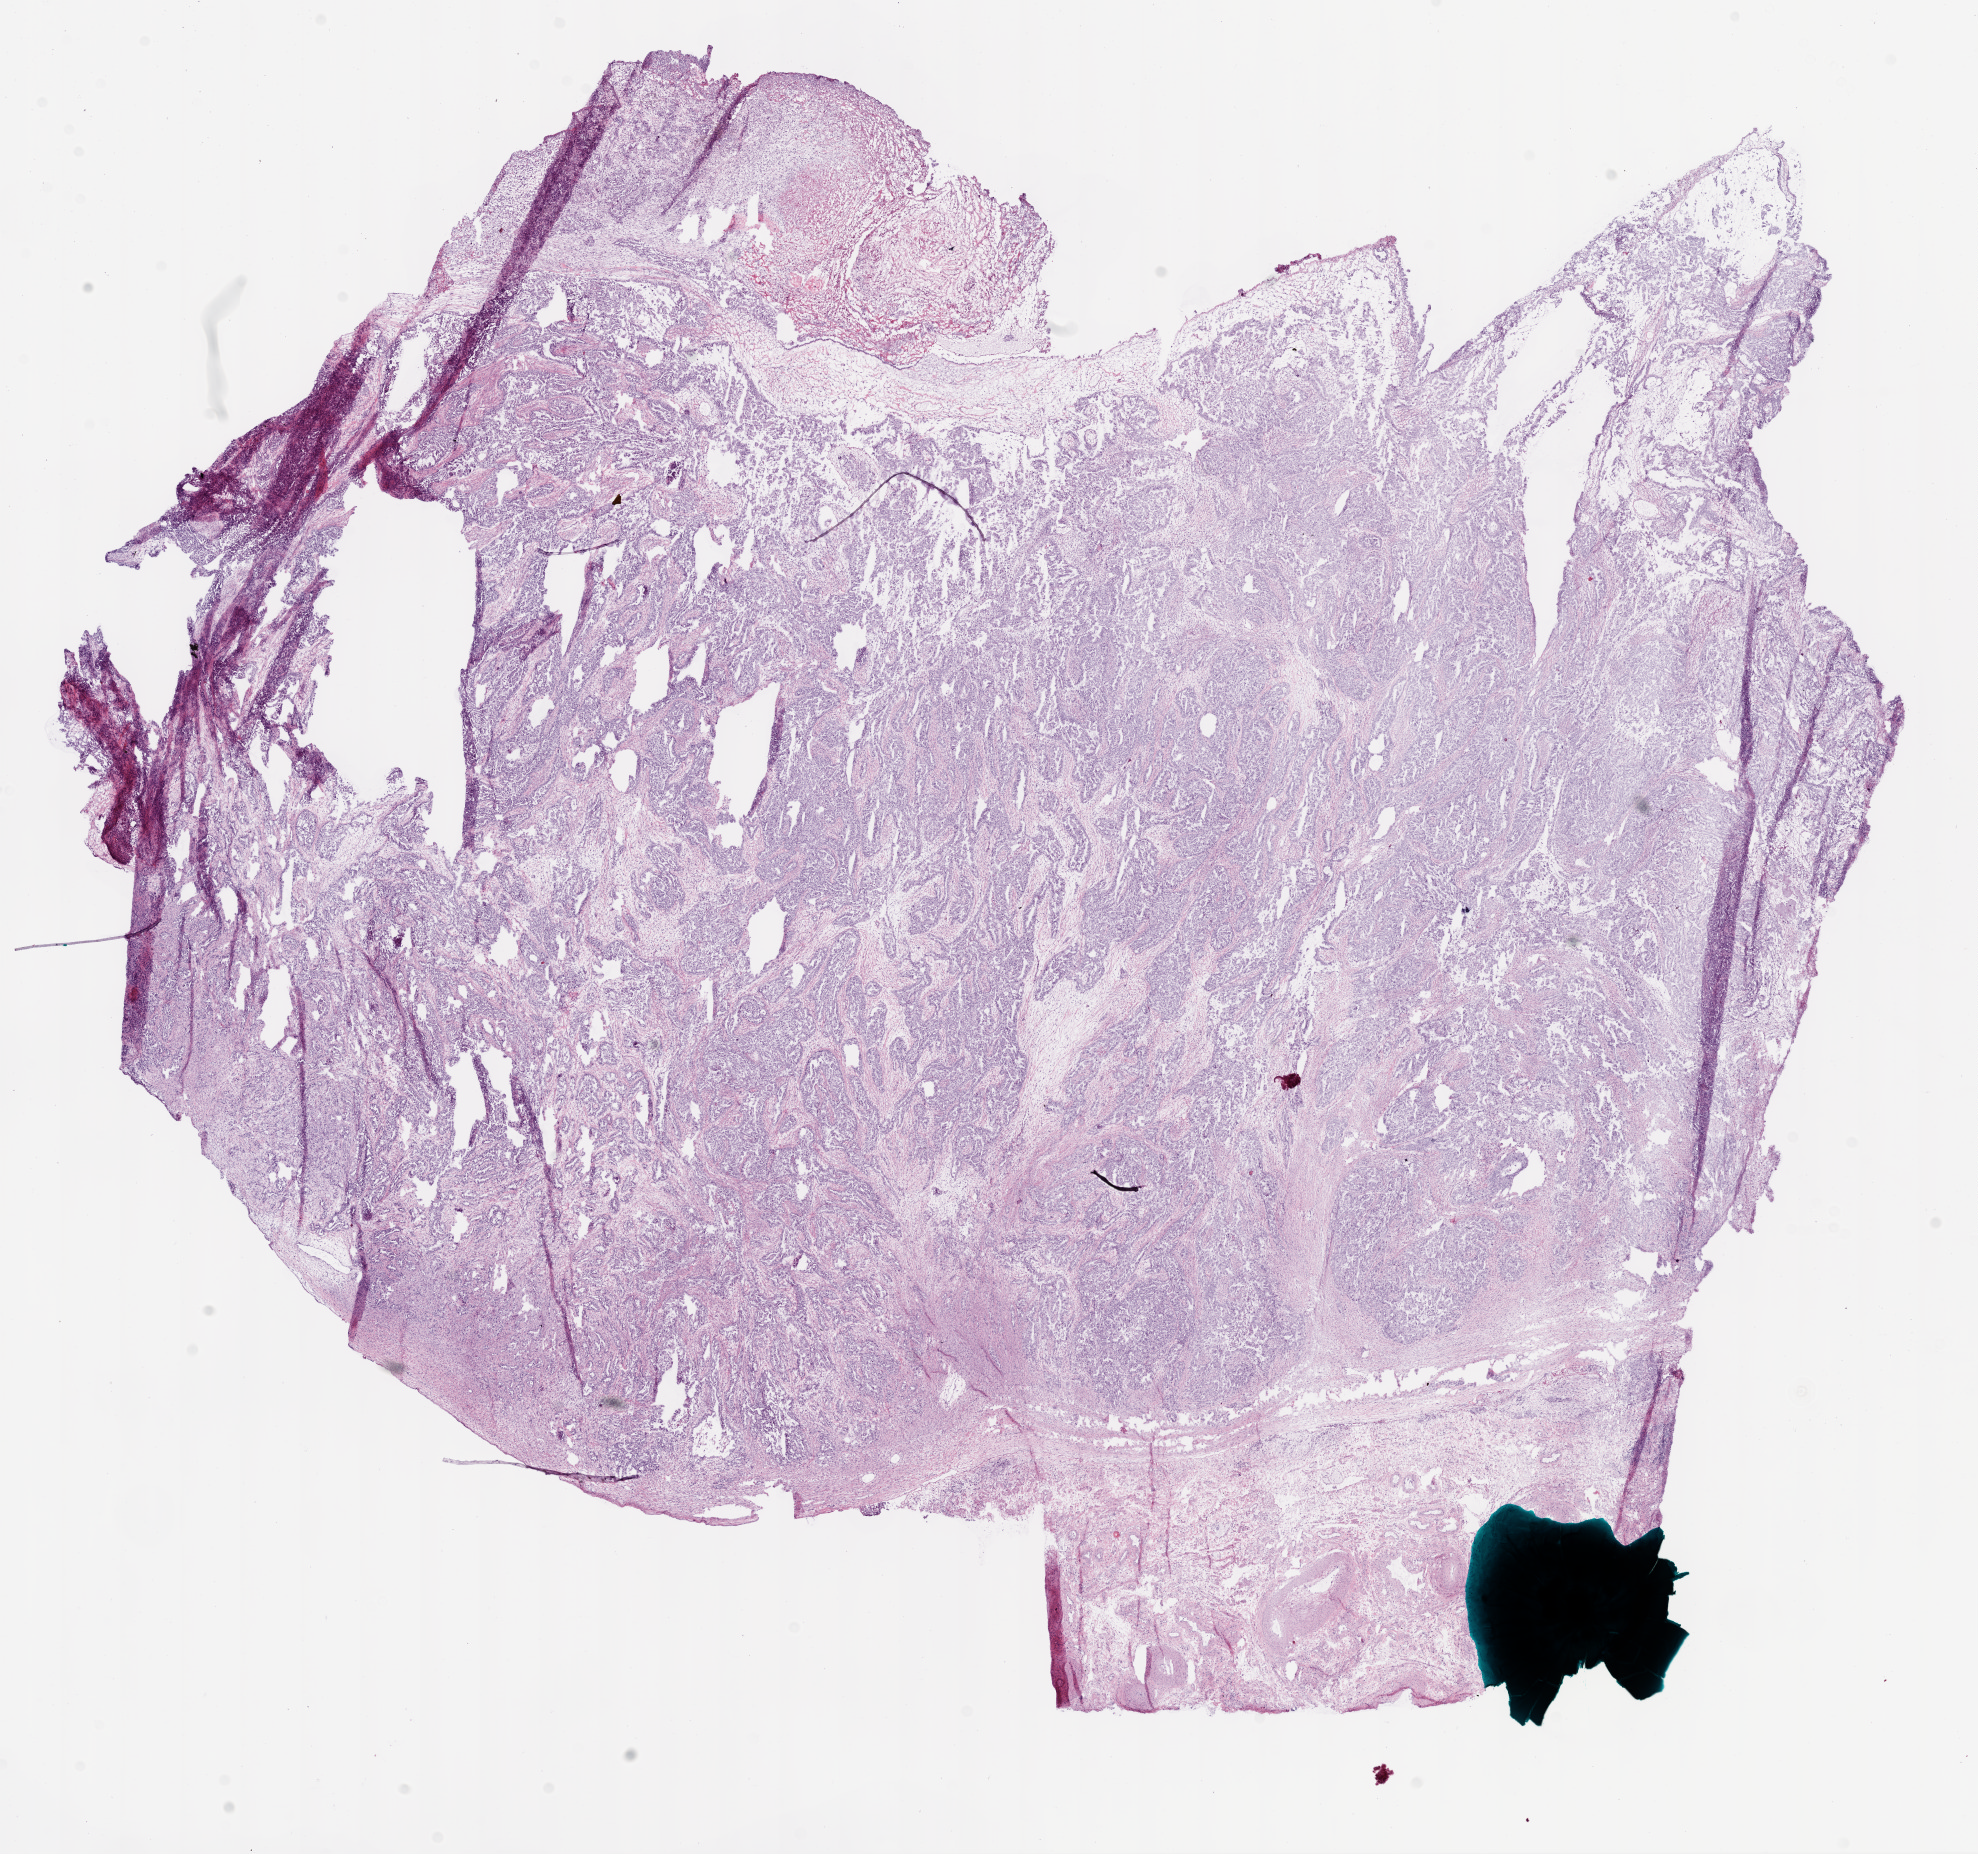
H&E-stained whole-slide image — shown as a low-resolution overview of the whole scanned area (about 16.0 x 15.0 mm), frozen section from the bottom of the tissue portion, primary tumour sample from the ovary. Female, age 62 years at initial diagnosis. Histologic grade: G3 (poorly differentiated). Slide review estimates, as recorded: tumour cells 80%, tumour nuclei 90%, normal cells 0%, stromal cells 20%, necrosis 0%.
* FIGO stage: IV
* laterality: bilateral
* pathologic diagnosis: Serous cystadenocarcinoma, NOS